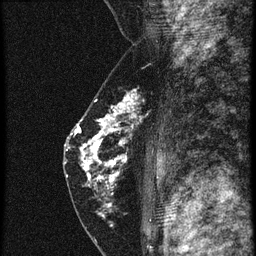
Breast MRI (dynamic contrast-enhanced), one sagittal slice; position 34 of 60 along the scan axis; 4 images stored at this slice position (order not interpretable as contrast timing); 1.5 T; TE 4.2 ms, TR 20.4 ms; 256 × 256 image matrix, field of view 180 × 180 mm. Patient: female, 46 years. From the clinical record (not read from this slice): setting: breast cancer imaged before/during neoadjuvant chemotherapy; receptor status: triple-negative.
Annotated regions visible in this slice (semi-automatically segmented with operator editing):
- analysis volume of interest (the breast-tissue region the enhancement analysis was run in; not a lesion): bounding box (x1, y1, x2, y2) in pixels: (67, 88, 153, 201)
- tumour enhancement mask (voxels above the 90 % enhancement threshold inside the analysis volume of interest): (69, 98, 137, 187)